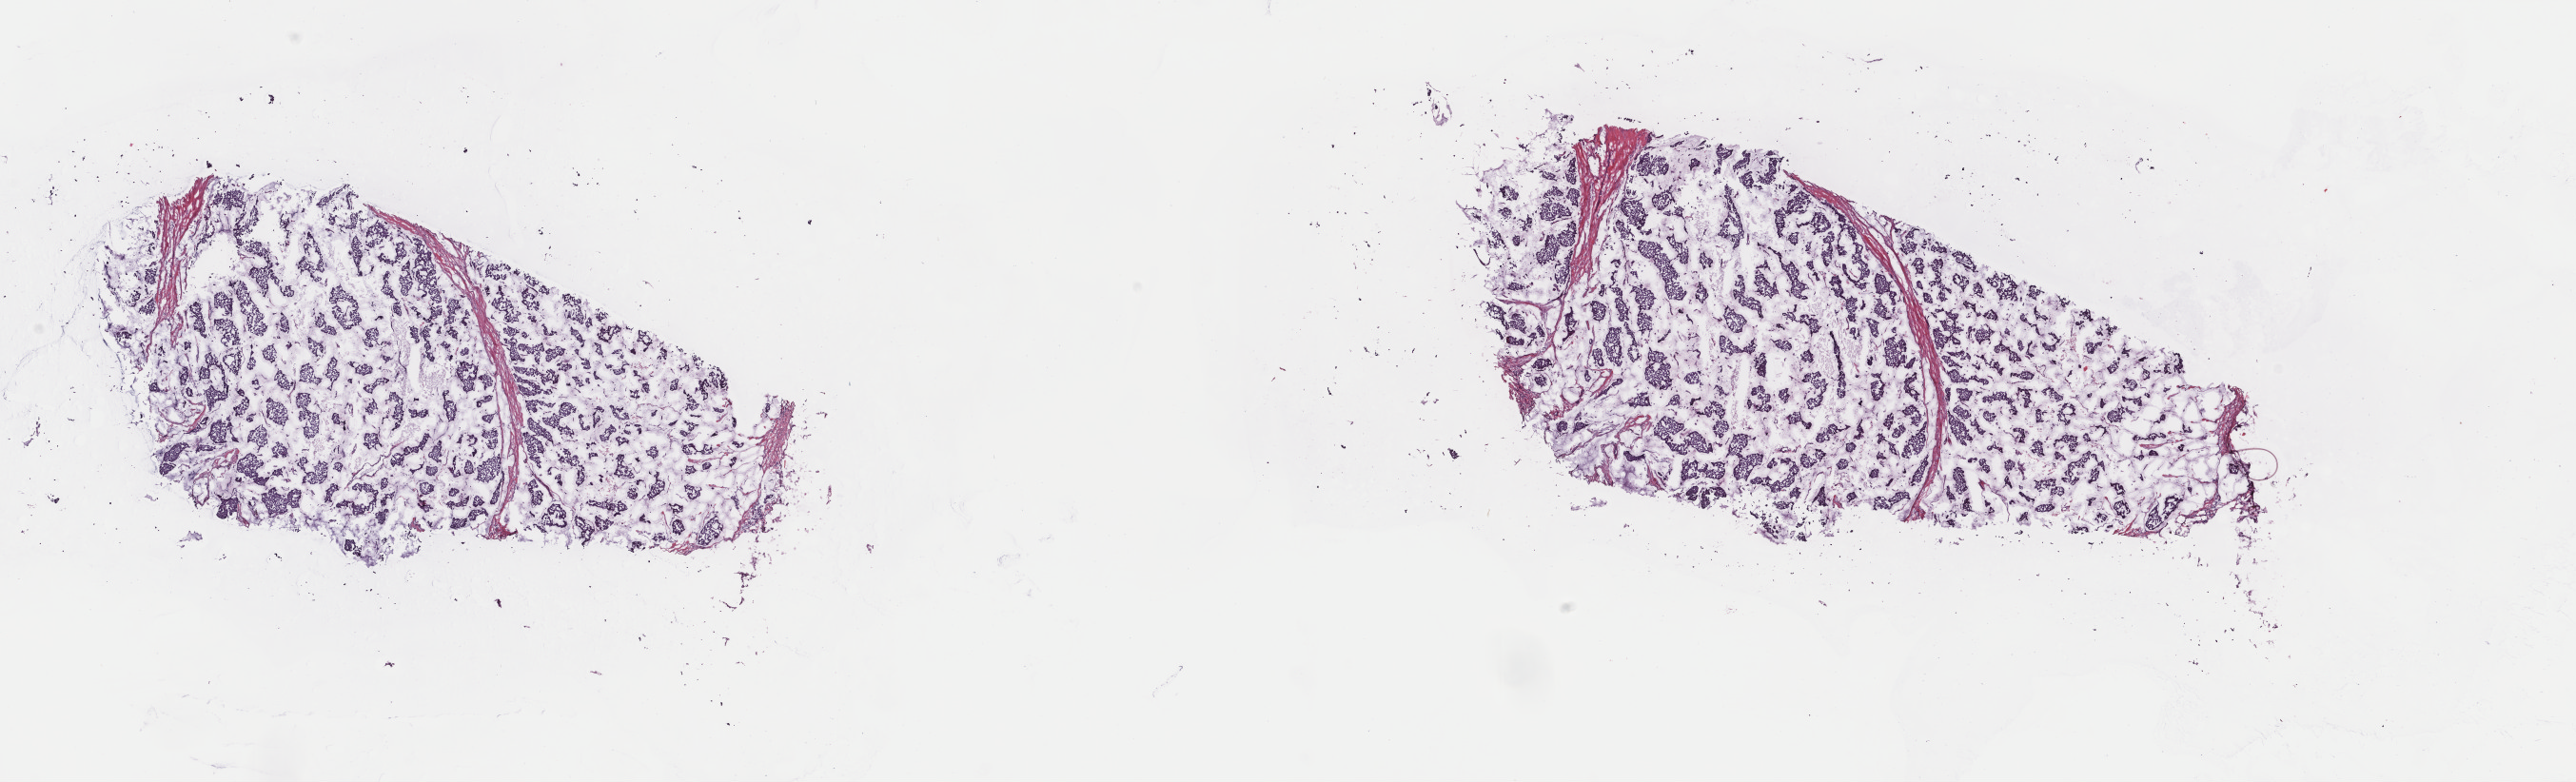
Digitized H&E-stained tissue section (whole slide), a low-resolution overview of the entire scanned area, about 21.5 x 6.5 mm, frozen section, breast, primary tumour sample. Patient: female, age at initial diagnosis 77 years. Composition of this section per pathologist review: tumour cells 80%, tumour nuclei 80%, normal cells 0%, stromal cells 20%, necrosis 0%. Inflammatory infiltration, as recorded: lymphocyte infiltration 40%, monocyte infiltration 25%, neutrophil infiltration 10%.
AJCC pathologic stage: IIA (7th edition). TNM: T2 N0 M0. Lymph nodes positive (case pathology): 0 of 1 examined. Histologic diagnosis: Mucinous adenocarcinoma.